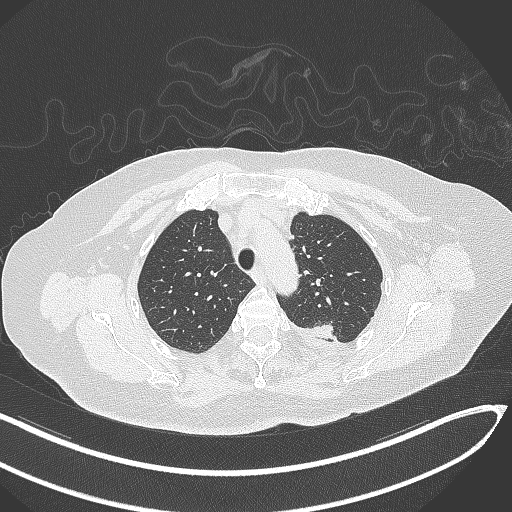
Chest CT, one axial slice; position 253 of 270 along the scan axis; reconstruction kernel B70f; lung window (W 1500 / L -600 HU); 1 mm slice thickness; 512 × 512 image matrix, field of view 400 × 400 mm. Female patient, age 76 years. Case-level facts recorded for this patient, not image findings: clinical TNM (as recorded): T1c N0 M0.
Annotated regions visible in this slice (rectangle marked by the reading radiologist):
- lung tumour (recorded histology: adenocarcinoma): bounding box [x1, y1, x2, y2] px = [308, 320, 334, 341]